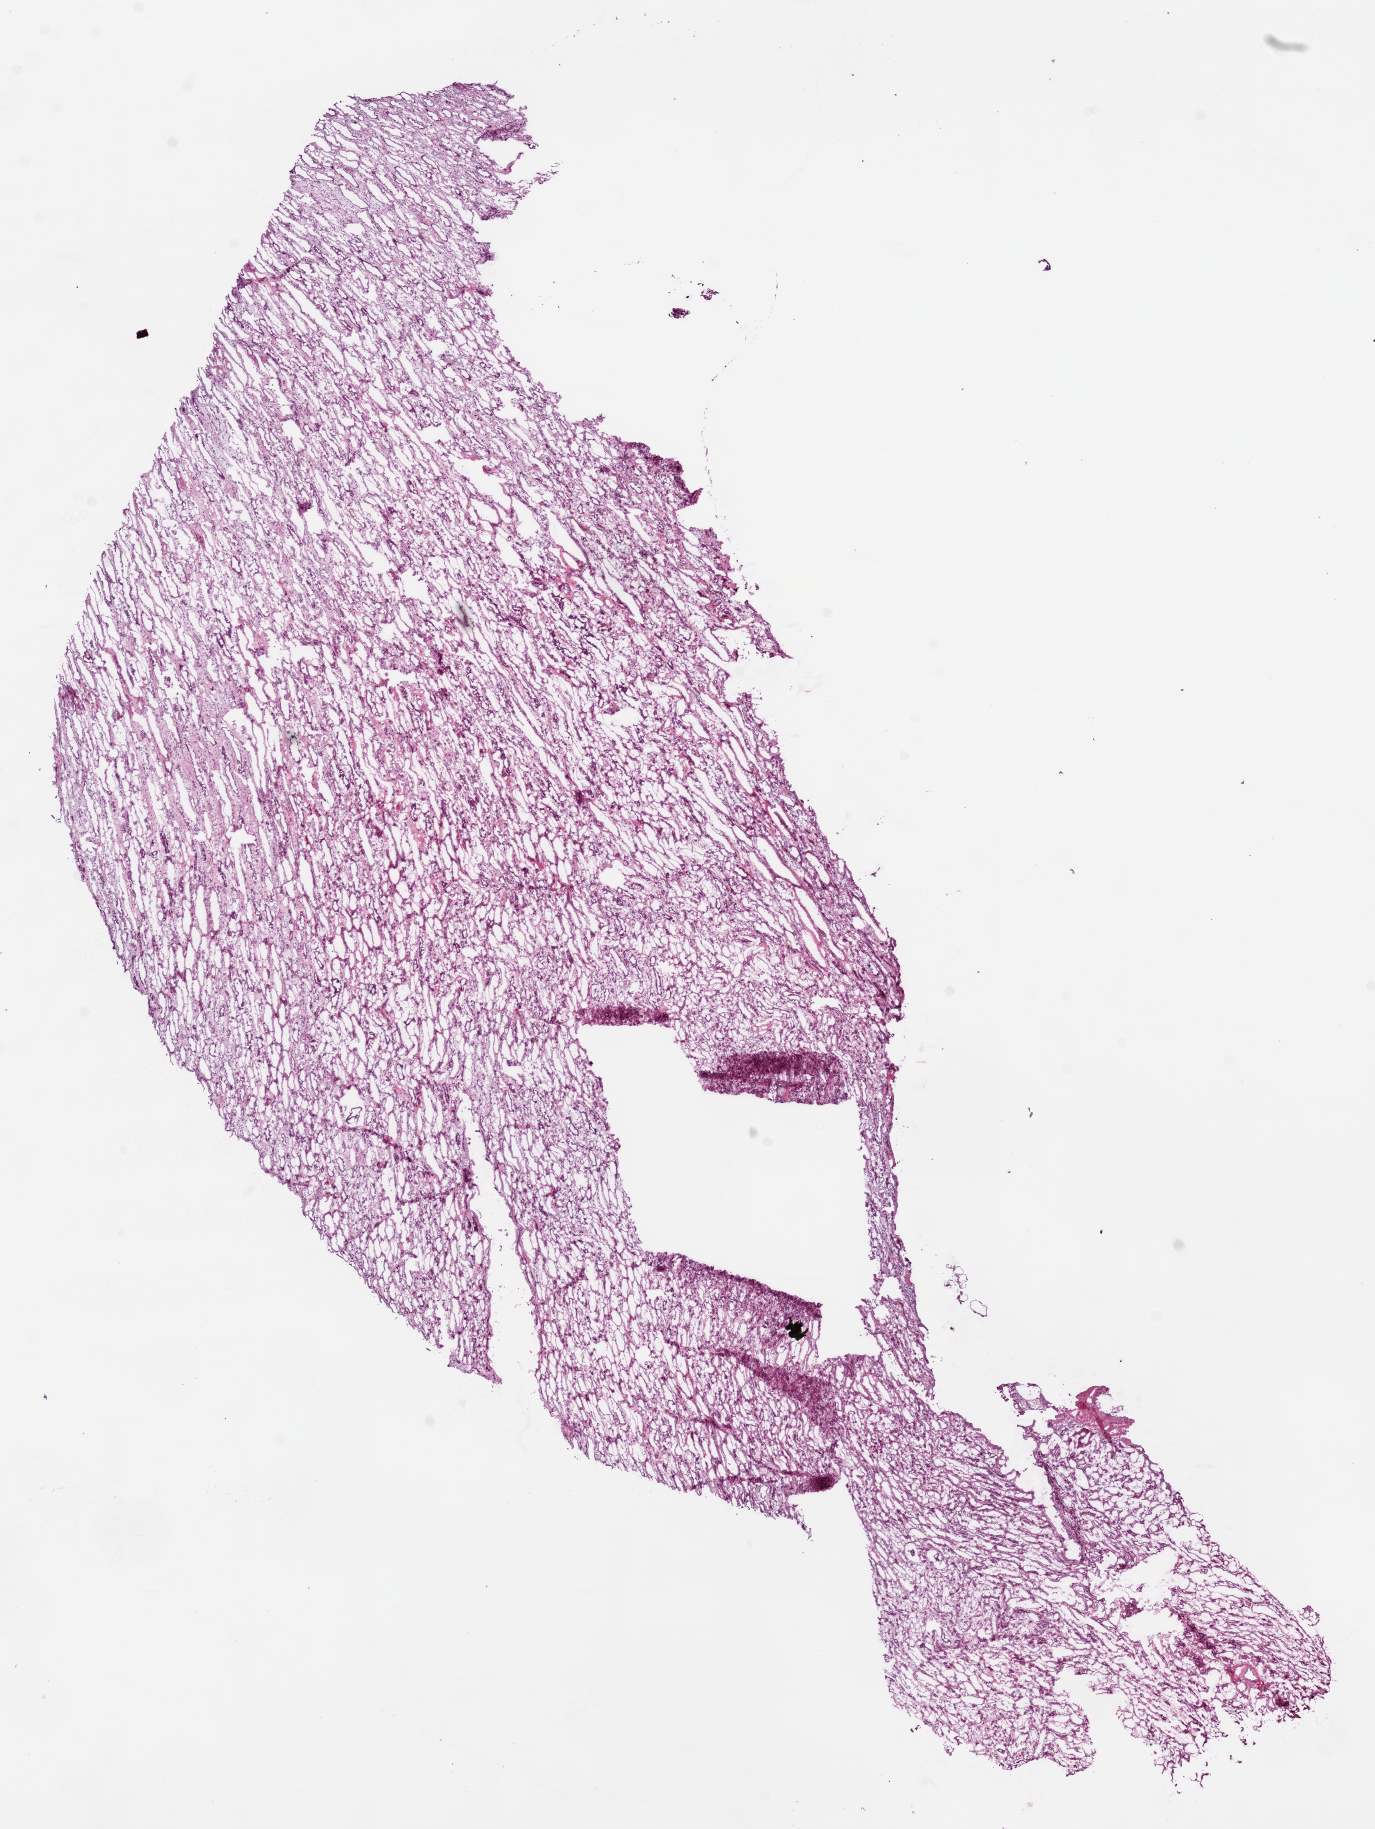
Digitized H&E tissue section (whole slide), low-resolution overview of the scanned area, about 11.0 x 14.7 mm (acquisition: 20x scan); frozen section; solid tissue normal (non-tumour tissue) sample from the kidney. Male patient; age at initial diagnosis 39 years.
* this section: solid tissue normal sample (biorepository sample class)
* patient diagnosis: Clear cell adenocarcinoma, NOS